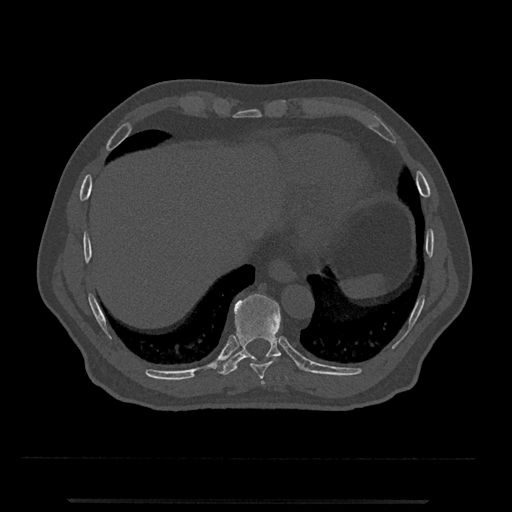
CT including the spine, one axial slice; position 543 of 797 along the scan axis; 120 kVp; bone window (W 1800 / L 400 HU); 0.5 mm slice thickness; 512 × 512 image matrix, field of view 419 × 419 mm. Male patient, age 63 years. Case-level facts recorded for this patient, not image findings: primary cancer: prostate.
Outlined on this slice (semi-automatic segmentation, software-assisted and operator-edited):
- T10 vertebra: bounding box (x1, y1, x2, y2) in pixels: (218, 294, 281, 375)
- T8 vertebra: (261, 381, 265, 385)
- T9 vertebra: (250, 356, 280, 379)